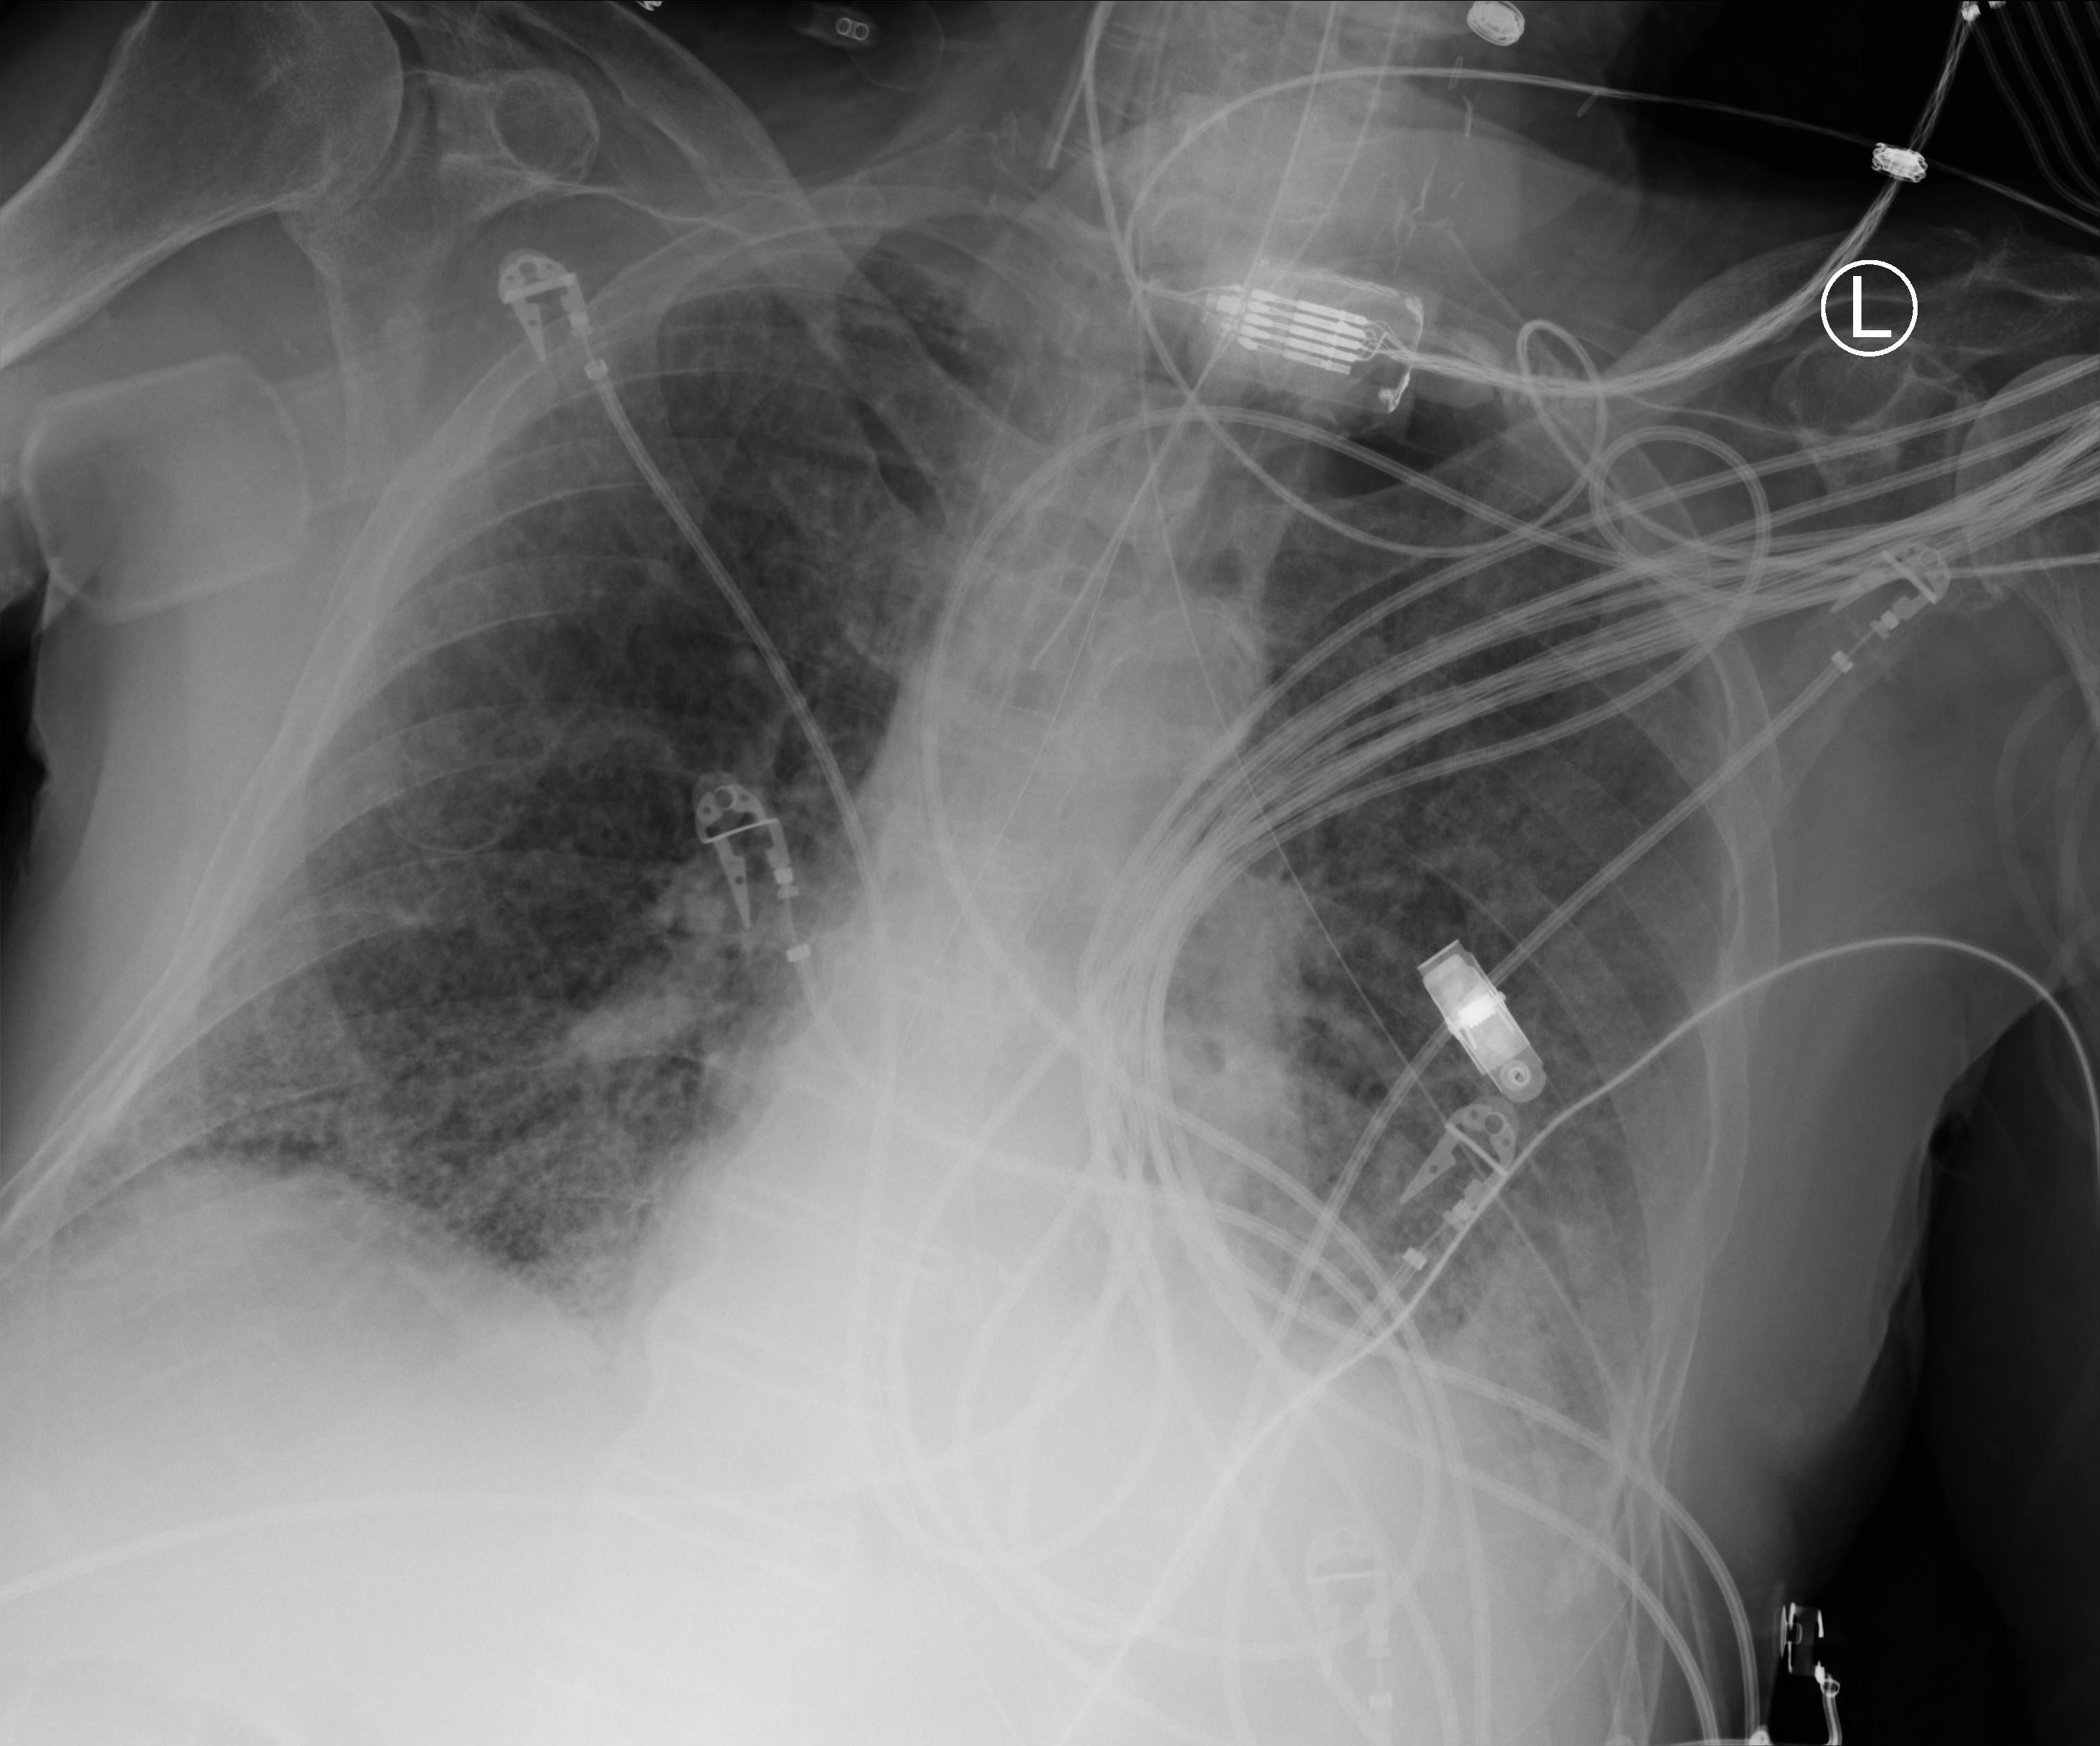
Chest X-ray (portable), anteroposterior (AP) projection. Patient hospitalised with COVID-19; male, aged 75–90 years.
From the hospital-stay record, not from the radiograph (when in the stay this image was taken is not recorded):
- admitted to intensive care during this hospital stay: yes
- length of hospital stay: 6 days
- mechanically ventilated during this hospital stay: yes